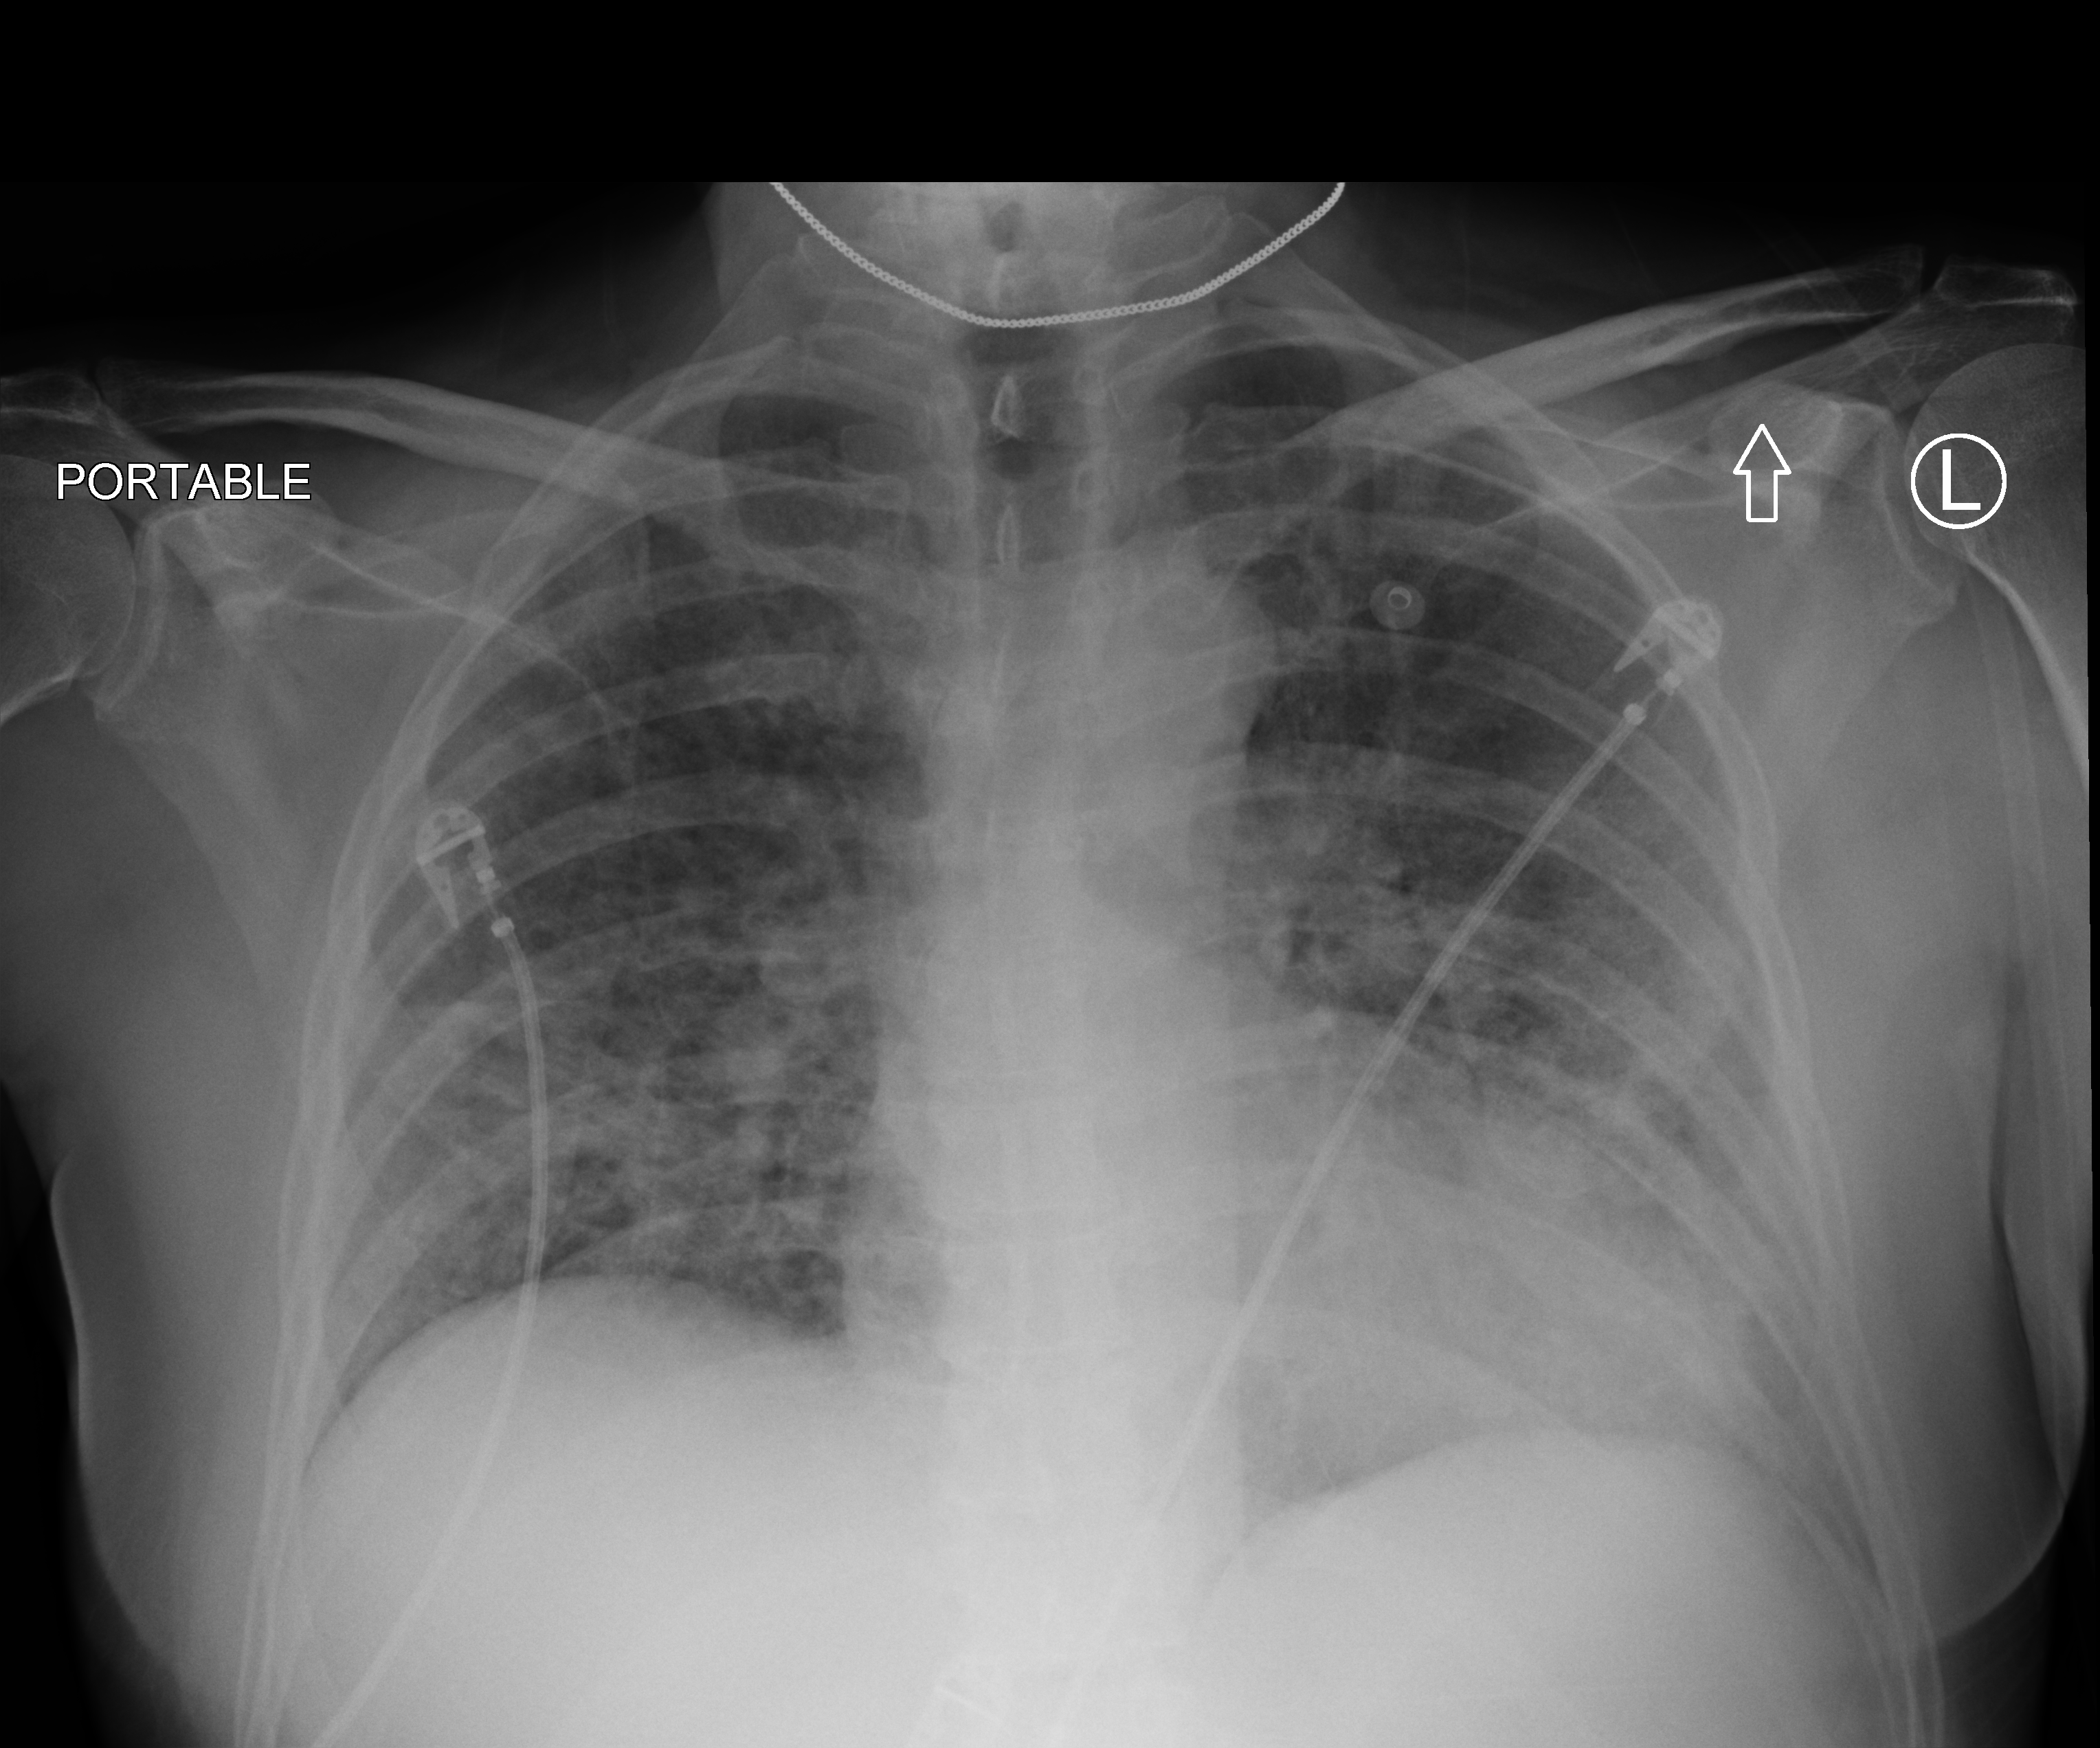
Portable chest radiograph, anteroposterior (AP) projection. Male patient hospitalised with COVID-19, age 60–74 years.
Hospital-stay facts (about this admission, not read from this image; timing relative to this image not recorded):
- other chronic lung disease (admission record): no